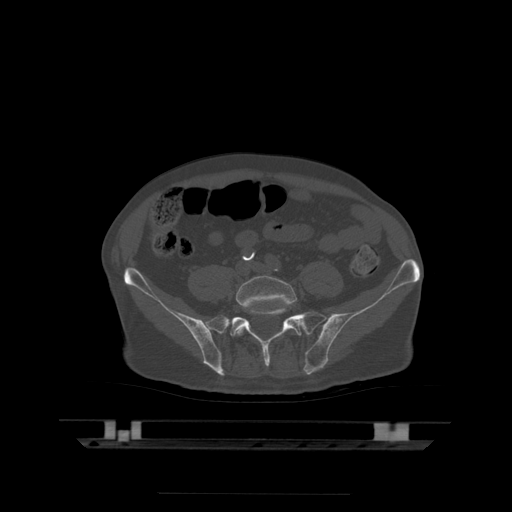
CT including the spine, one axial slice; position 63 of 522 along the scan axis; bone window (W 1800 / L 400 HU); 1.25 mm slice thickness; 512 × 512 image matrix. Patient age 68 years. From the clinical record (not read from this slice): primary cancer: urothelial.
Structures marked on this image (semi-automatically segmented with operator editing):
- L5 vertebra: bounding box (x1, y1, x2, y2) in pixels: (236, 276, 297, 336)